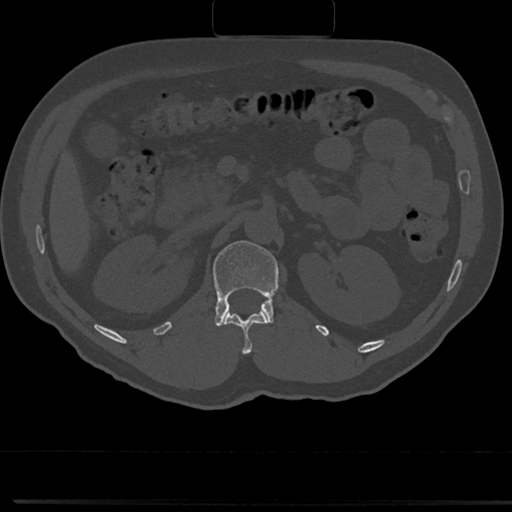
CT including the spine, one axial slice. Reconstruction kernel Br40s/3. 120 kVp. Bone window (W 1800 / L 400 HU). 0.5 mm slice thickness. 512 × 512 image matrix. Male patient, age 61 years. From the clinical record (not read from this slice): primary cancer: prostate.
Annotated regions visible in this slice (semi-automatically segmented with operator editing):
- L1 vertebra: box from (x=191, y=240) to (x=278, y=327) px
- T12 vertebra: (x=225, y=312)–(x=268, y=352)